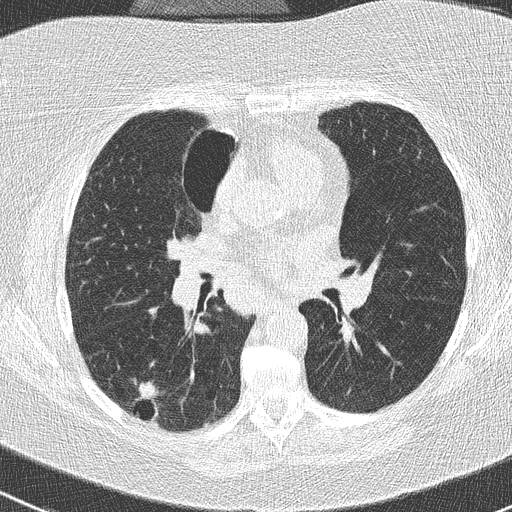
Chest CT (low-dose screening protocol), one axial image. Baseline annual screen. Lung window (W 1500 / L -600 HU). Slice 122 of 261 in the series. 512 × 512 image matrix. Female participant, aged 74 years at enrolment. Former smoker at enrolment.
Expert reader's lesion annotation, box from (x=121, y=374) to (x=175, y=431) px. The screening reader recorded 3 non-calcified nodules or masses ≥4 mm on this exam; which of them this box marks is not recorded. Official screen result: positive, change unspecified: nodule(s) >= 4 mm or enlarging nodule(s), mass(es), or other non-specific abnormalities suspicious for lung cancer. Participant outcome: lung cancer diagnosed 16 days after this screen — non-small cell carcinoma, right lower lobe, poorly differentiated (G3), stage IIIA (AJCC 6th edition), 28 mm at pathology.